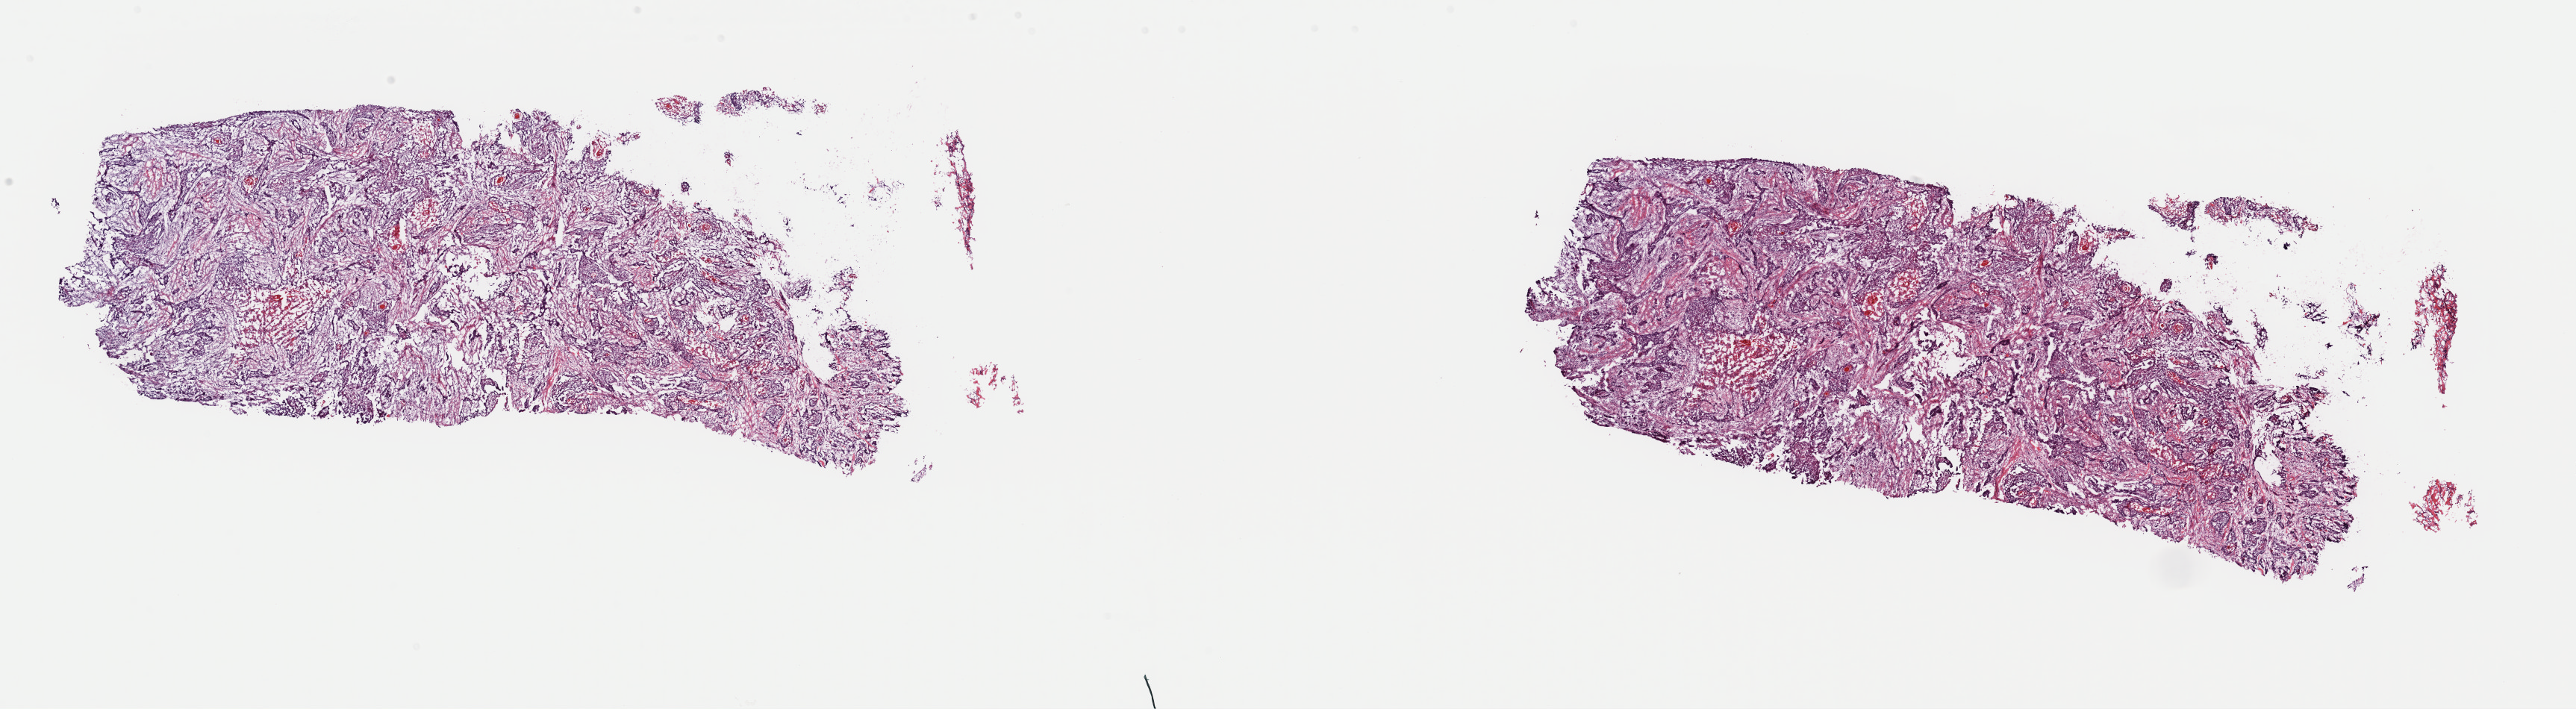
Whole-slide histology image, H&E-stained, a low-resolution overview of the entire scanned area, about 27.3 x 7.5 mm (acquisition: 40x scan); frozen section; esophagus, primary tumour sample. Patient: male, age at initial diagnosis 59 years. Histologic grade: G2 (moderately differentiated). Composition of this section per pathologist review: tumour cells 45%, tumour nuclei 75%, normal cells 0%, stromal cells 45%, necrosis 10%. Infiltration values recorded for this section: lymphocyte infiltration 12%, monocyte infiltration 3%, neutrophil infiltration 2%.
Pathologic diagnosis: Squamous cell carcinoma, NOS (middle third of esophagus). AJCC pathologic stage: IIA (6th edition).